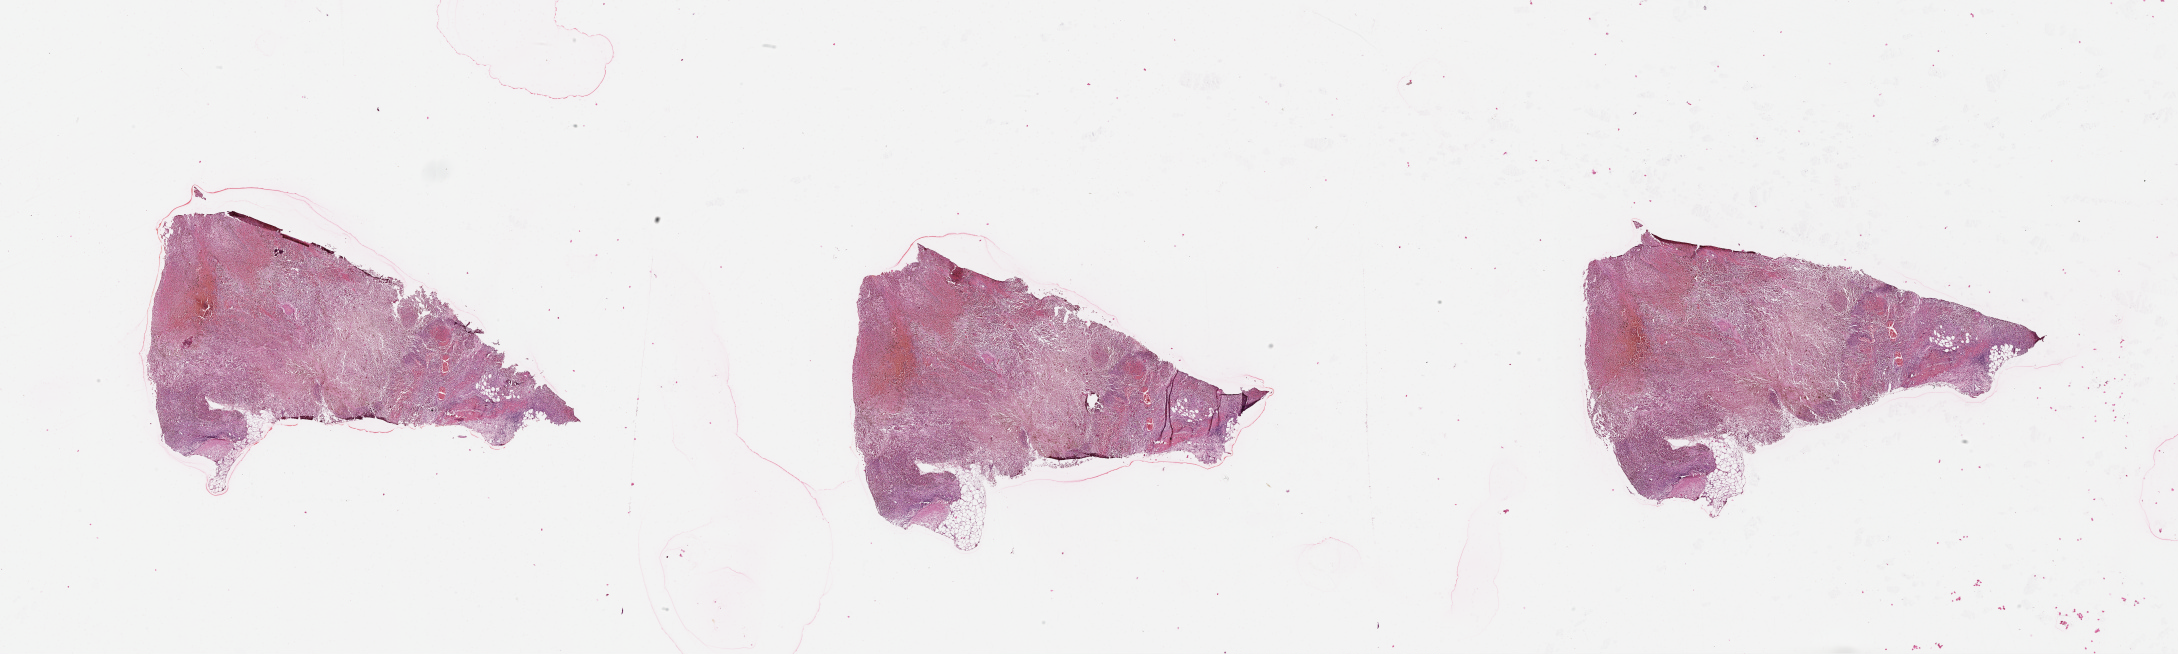
Hematoxylin and eosin (H&E) stained whole-slide image — shown as a low-resolution overview of the whole scanned area (about 35.1 x 10.5 mm). Female, 76 y/o.
Patient diagnosis: Malignant melanoma, NOS.